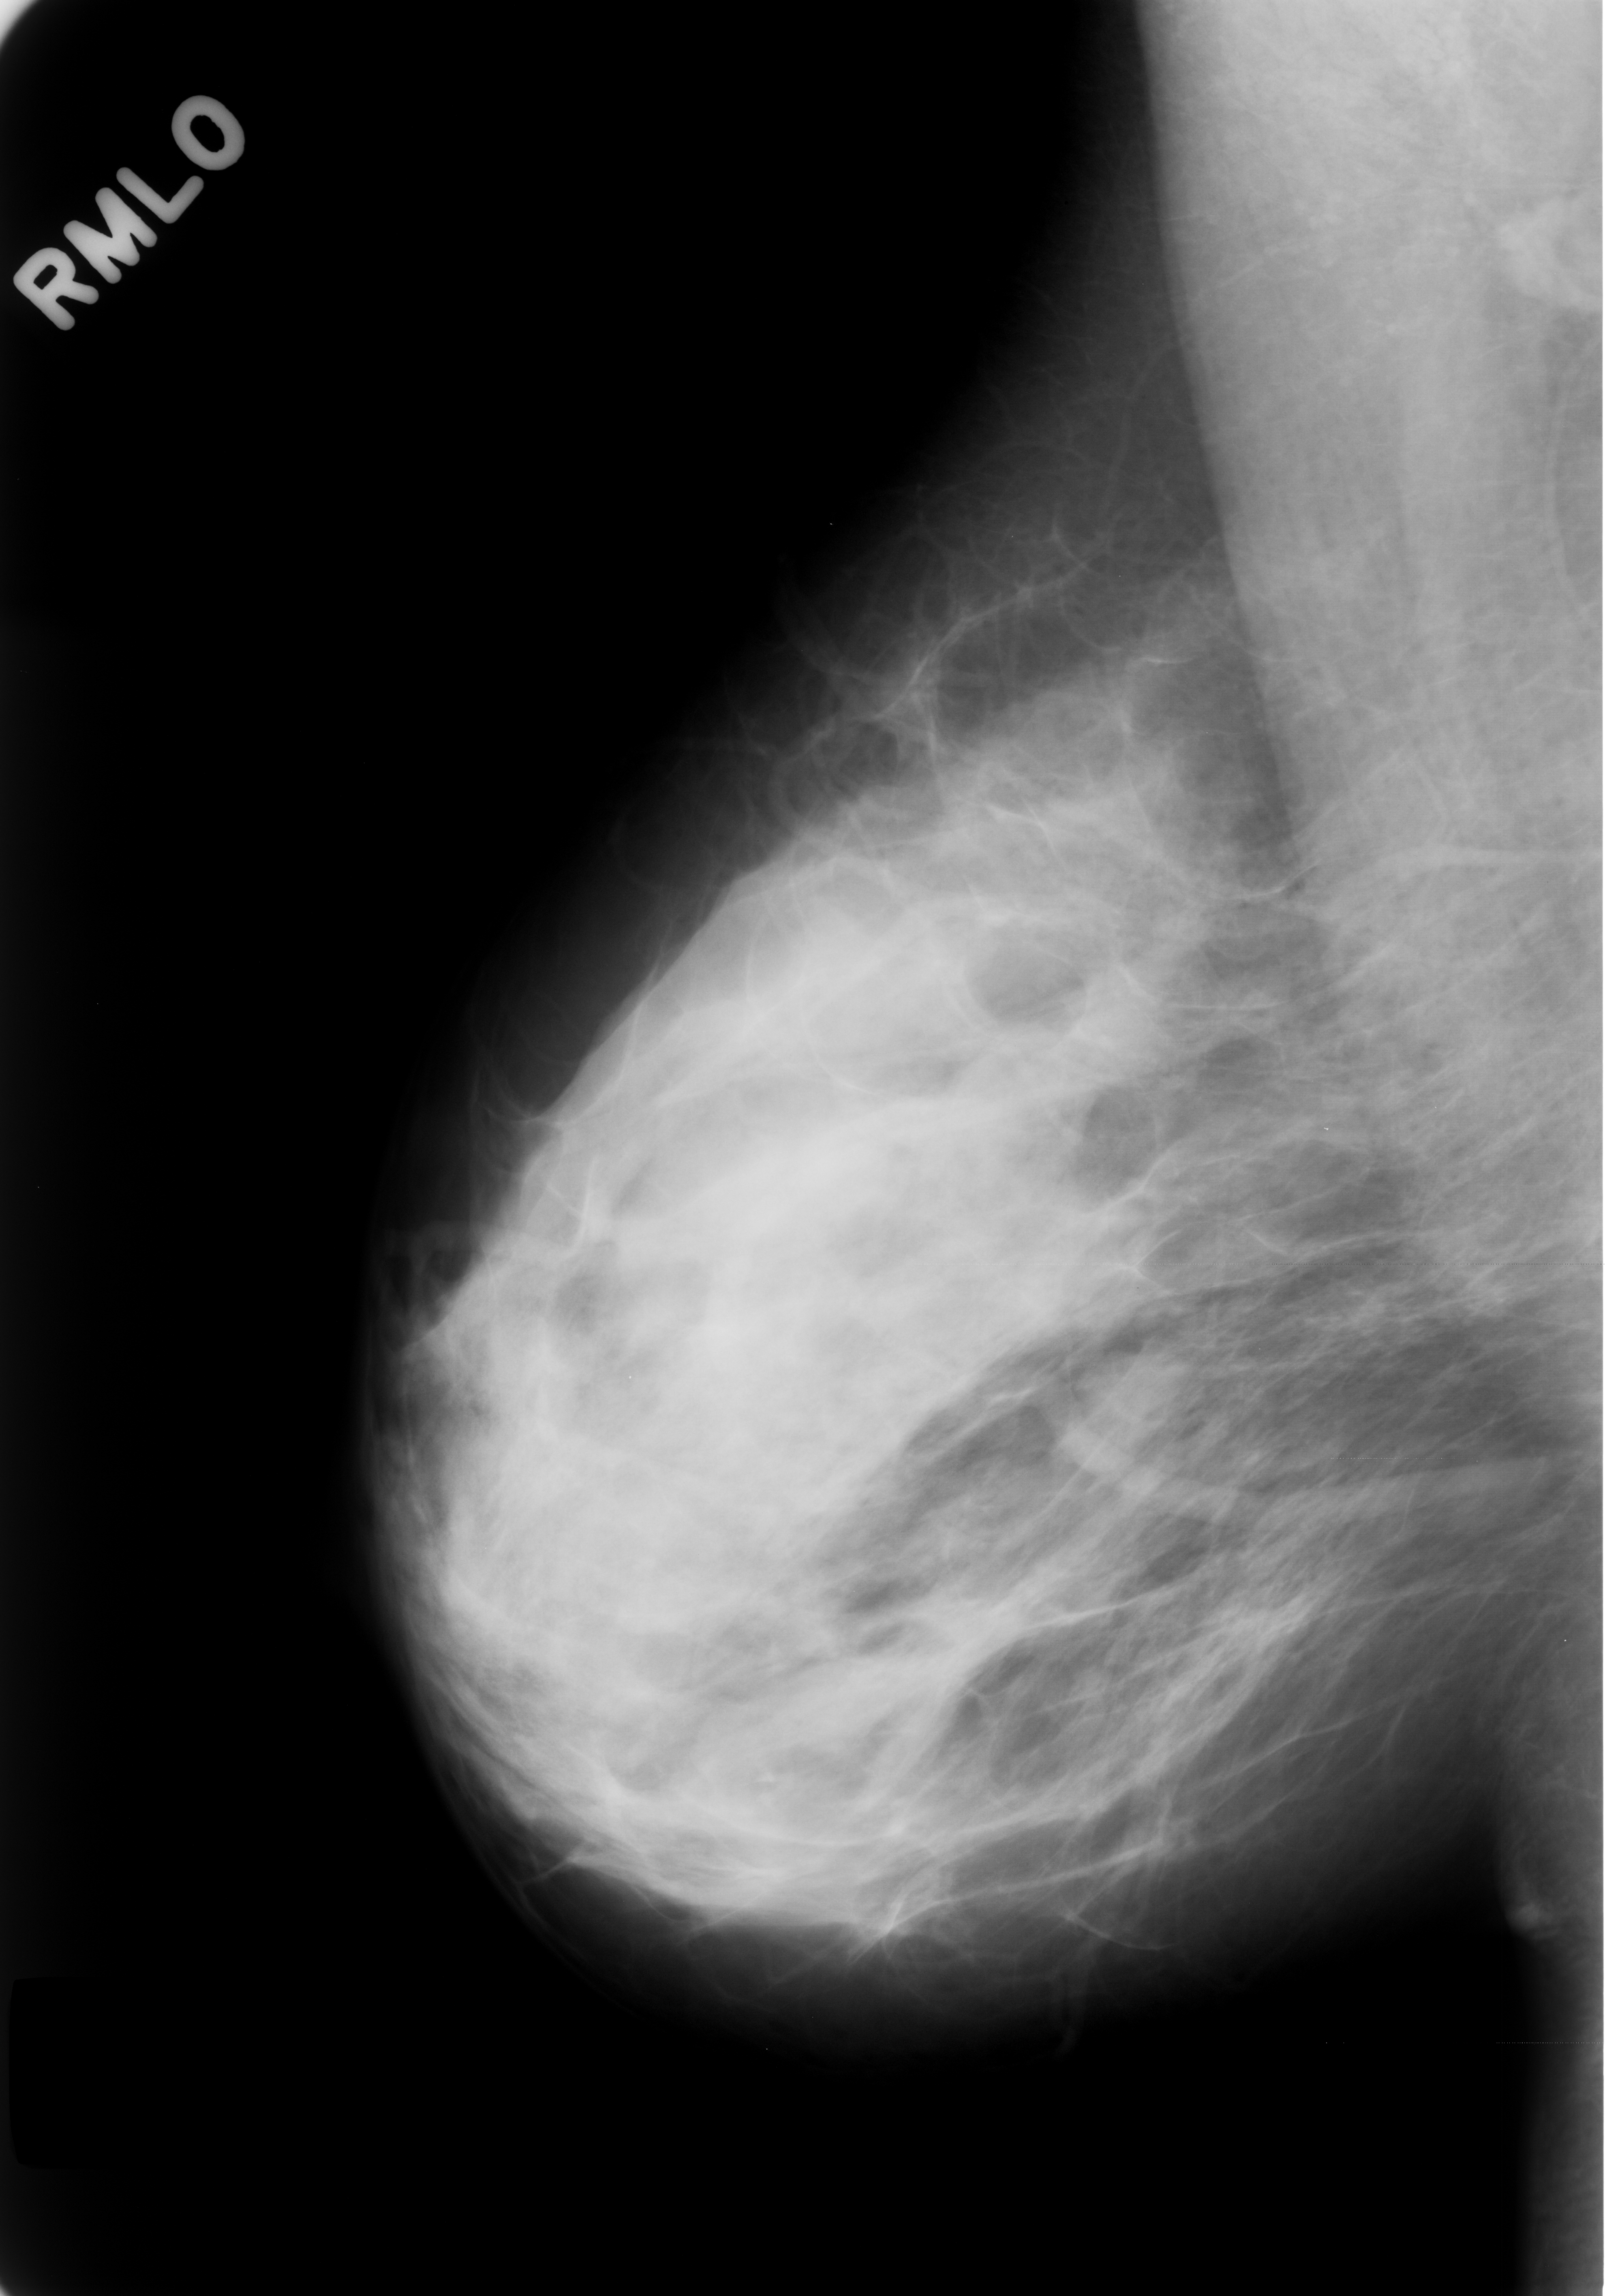
Scanned film-screen mammogram, right breast, mediolateral oblique (MLO) view, BI-RADS breast density category 3 (scale 1–4).
Marked abnormality: mass, shape lobulated, margins obscured; BI-RADS assessment category 3; subtlety rating 3 on a 1 (subtle) to 5 (obvious) scale; benign without callback (not worked up further).